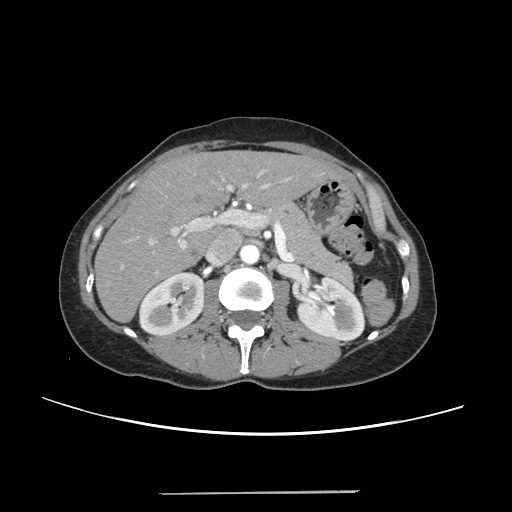
Contrast-enhanced abdominal CT, one axial slice; position 133 of 240 along the scan axis; intravenous contrast given; soft-tissue window (W 400 / L 40 HU); 1.25 mm slice thickness; 512 × 512 image matrix, field of view 371 × 371 mm. Female patient, age 60 years. Case-level facts recorded for this patient, not image findings: diagnosis: colorectal cancer liver metastases, imaged before liver resection; multiple liver metastases: no.
Structures marked on this image (manually delineated by an expert):
- liver: bounding box (x1, y1, x2, y2) in pixels: (96, 152, 335, 321)
- planned liver remnant (the part of the liver to remain after resection): (96, 152, 335, 321)
- portal vein (with intrahepatic branches): (121, 170, 290, 274)